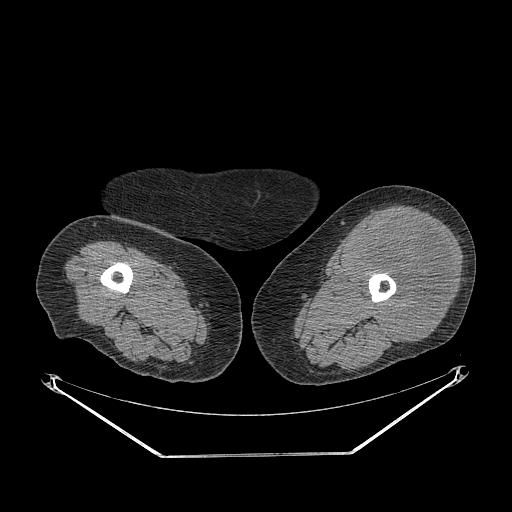
CT of an extremity soft-tissue mass (from a PET/CT study), one axial slice; position 225 of 267 along the scan axis; reconstruction kernel STANDARD; soft-tissue window (W 400 / L 40 HU); 3.75 mm slice thickness; 512 × 512 image matrix. Female patient. From the clinical record (not read from this slice): histological type: undifferentiated – high grade; grade: high; site of the primary tumour: left thigh.
Structures marked on this image (expert contour drawn on MRI and transferred to this co-registered scan by the dataset authors):
- gross tumour volume including surrounding oedema: bounding box <354,217,453,341> (left, top, right, bottom; pixels)
- gross tumour volume (mass): <354,217,453,341>